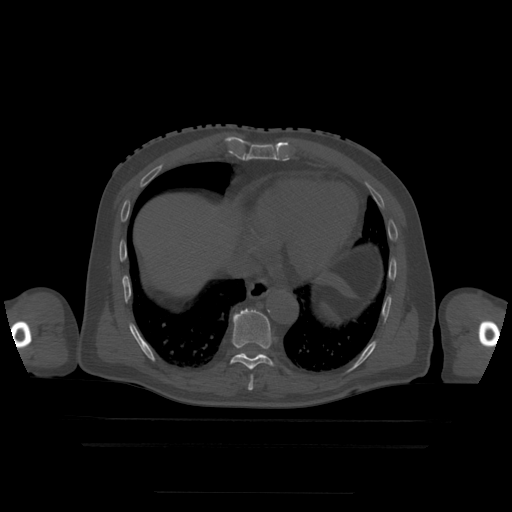
CT including the spine, one axial slice. Position 260 of 522 along the scan axis. Bone window (W 1800 / L 400 HU). 1.25 mm slice thickness. 512 × 512 image matrix, field of view 436 × 436 mm. Patient age 68 years. Case-level facts recorded for this patient, not image findings: primary cancer: urothelial.
Outlined on this slice (semi-automatic segmentation, software-assisted and operator-edited):
- T10 vertebra: bounding box <261,354,264,356> (left, top, right, bottom; pixels)
- T7 vertebra: <248,387,250,390>
- T8 vertebra: <249,376,254,390>
- T9 vertebra: <231,309,274,371>